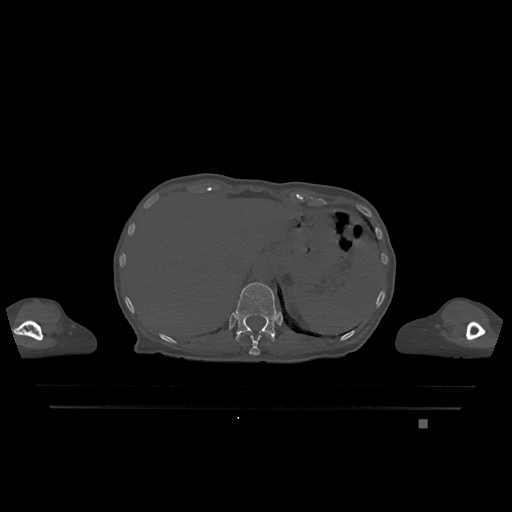
CT including the spine, one axial slice; slice 550 of 1317 in the series (ordered by position); bone window (W 1800 / L 400 HU); 0.5 mm slice thickness; 512 × 512 image matrix, field of view 500 × 500 mm. Female patient, age 74 years. Case-level facts recorded for this patient, not image findings: primary cancer: lung.
Structures marked on this image (semi-automatic segmentation, software-assisted and operator-edited):
- T11 vertebra: bounding box (x1, y1, x2, y2) in pixels: (249, 333, 271, 355)
- T12 vertebra: (235, 282, 278, 341)